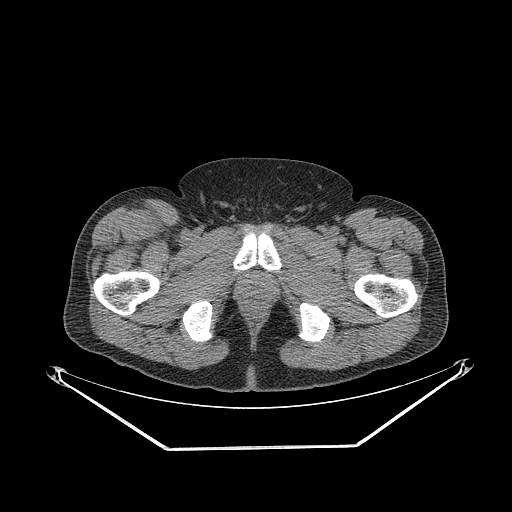
CT of an extremity soft-tissue mass (from a PET/CT study), one axial slice. Slice 310 of 311 in the series (ordered by position). 140 kVp. Soft-tissue window (W 400 / L 40 HU). 3.75 mm slice thickness. 512 × 512 image matrix, field of view 500 × 500 mm. Male patient. Case-level facts recorded for this patient, not image findings: histological type: pleiomorphic leiomyosarcoma; grade: intermediate; site of the primary tumour: right thigh.
Annotated regions visible in this slice (expert contour drawn on MRI and transferred to this co-registered scan by the dataset authors):
- gross tumour volume including surrounding oedema: box from (x=148, y=215) to (x=161, y=229) px